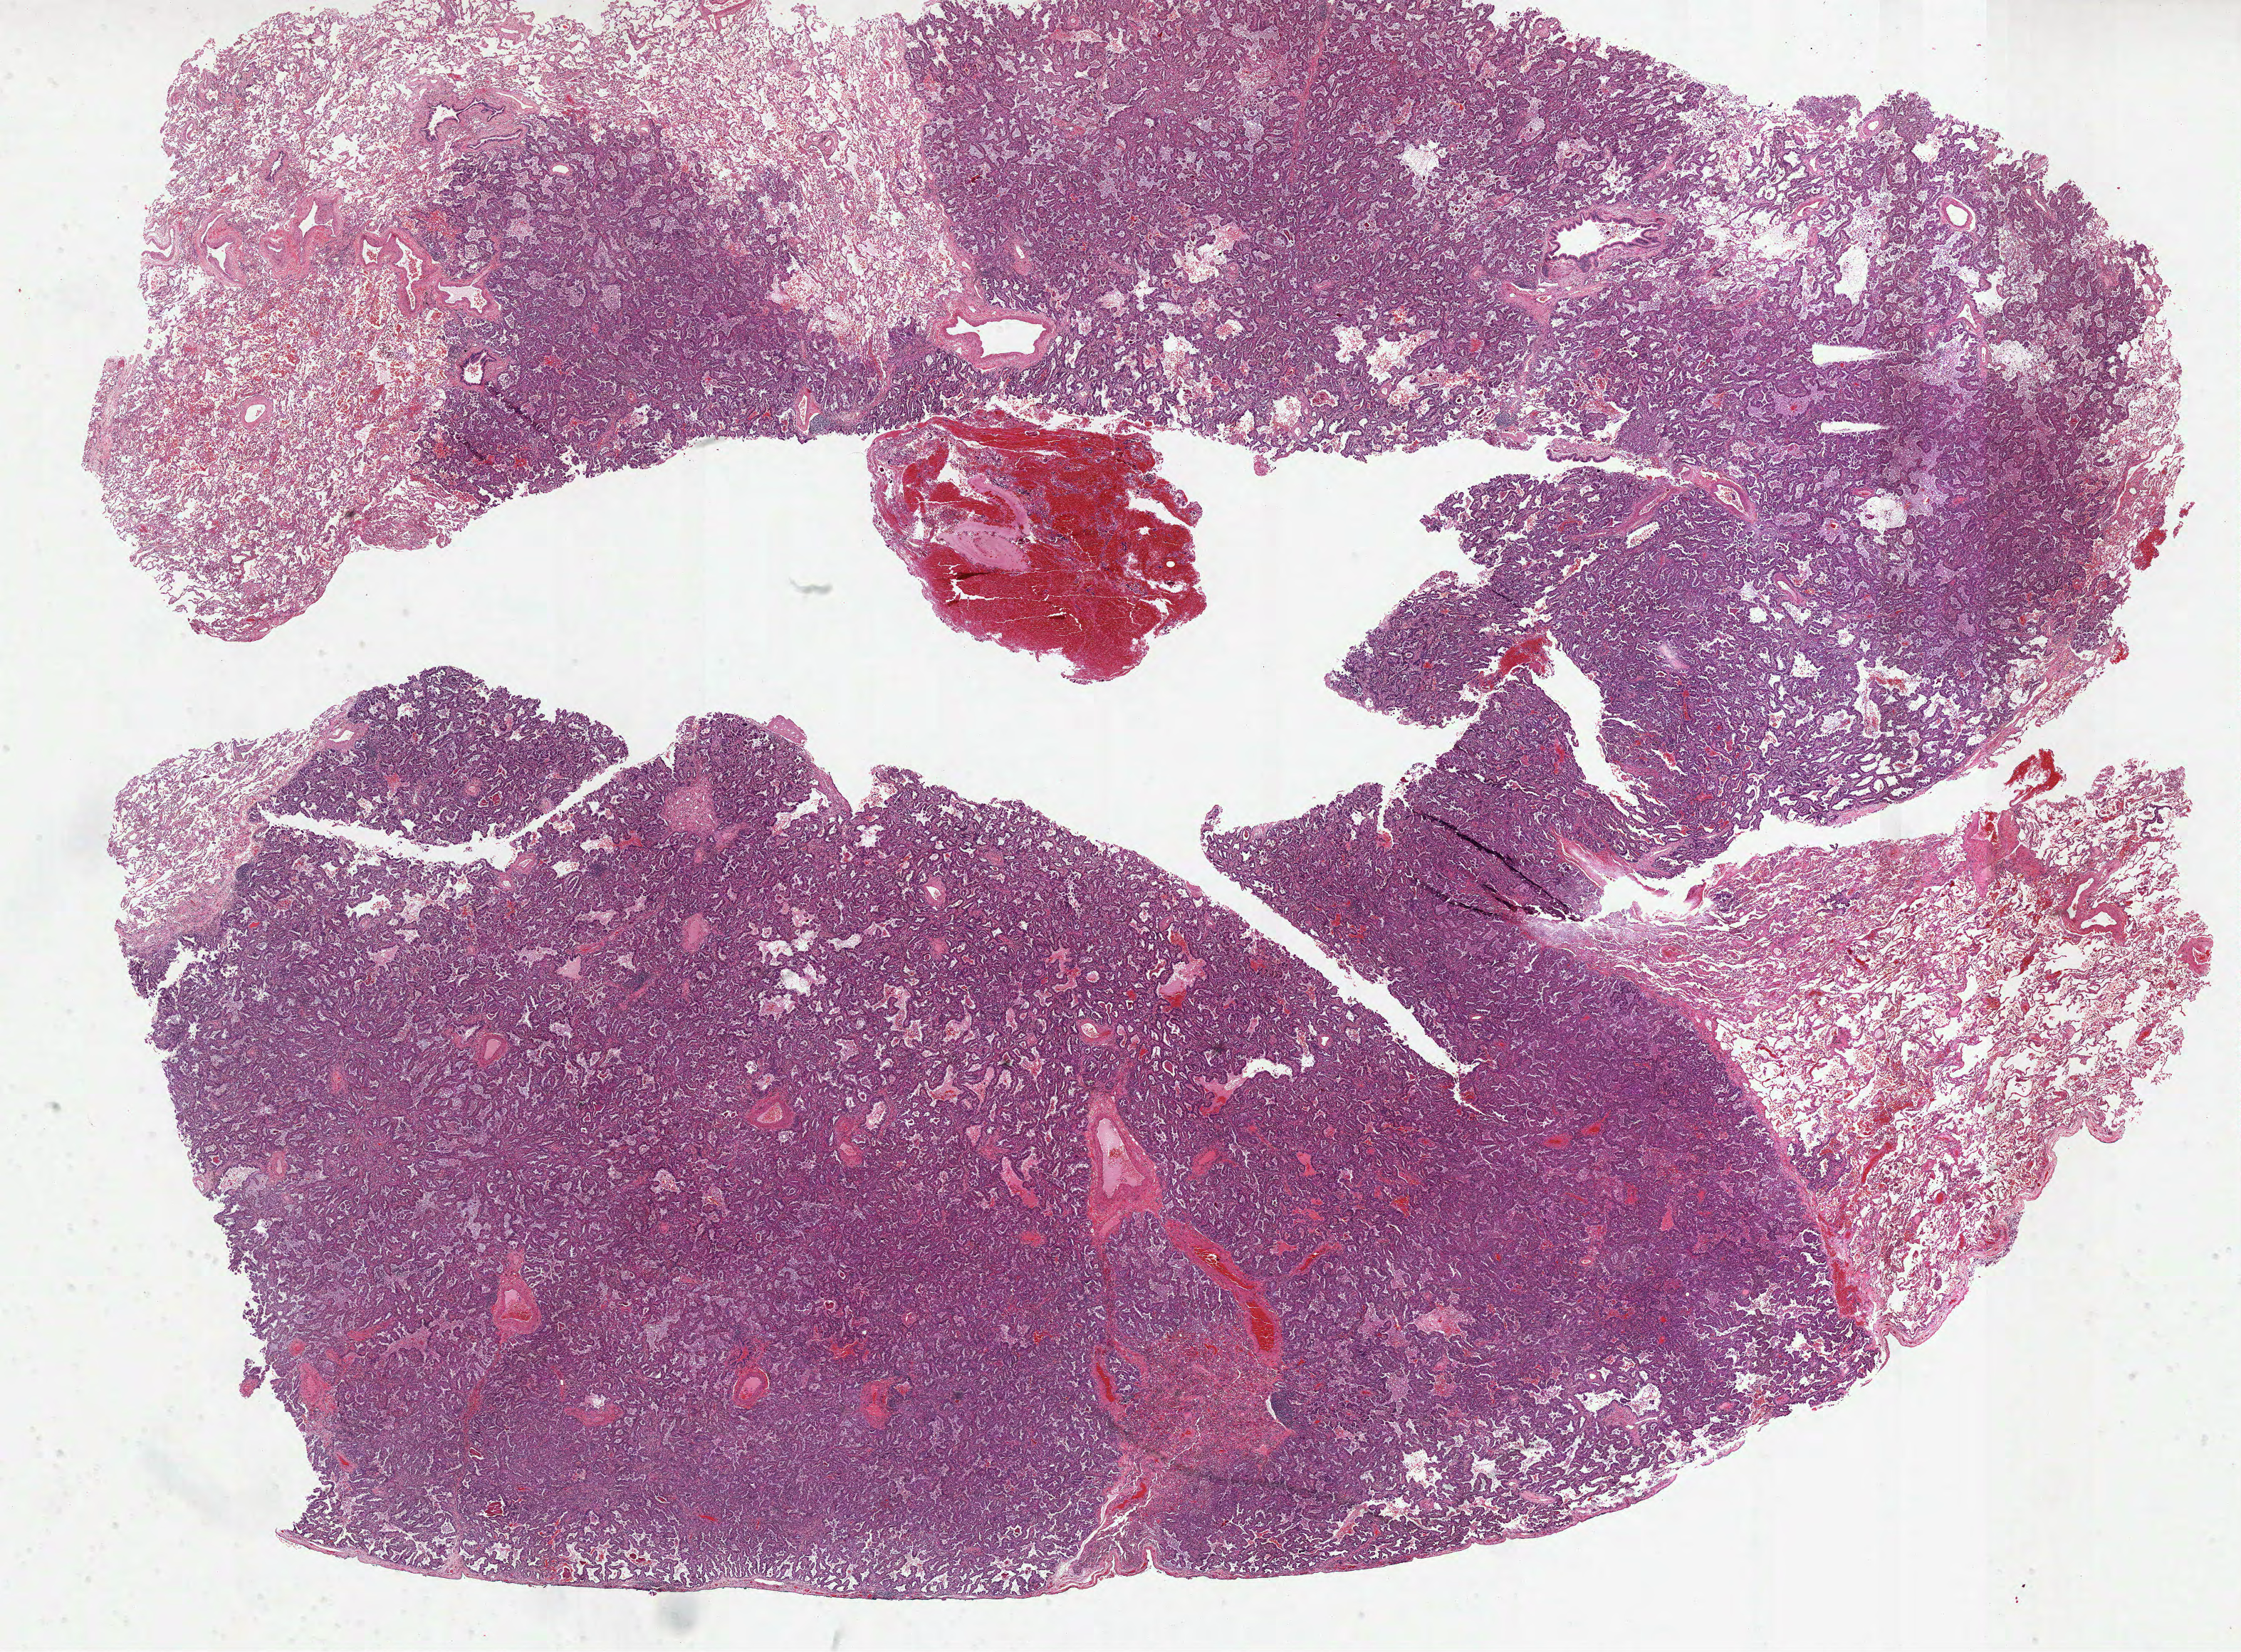
Hematoxylin and eosin (H&E) stained whole-slide image — whole scanned area (about 25.4 x 18.7 mm) shown as a low-resolution overview. Formalin-fixed paraffin-embedded (FFPE) diagnostic section. Sample: primary tumour, lung. Female patient; age at initial diagnosis 67 years.
Diagnosis: Adenocarcinoma, NOS (upper lobe, lung).